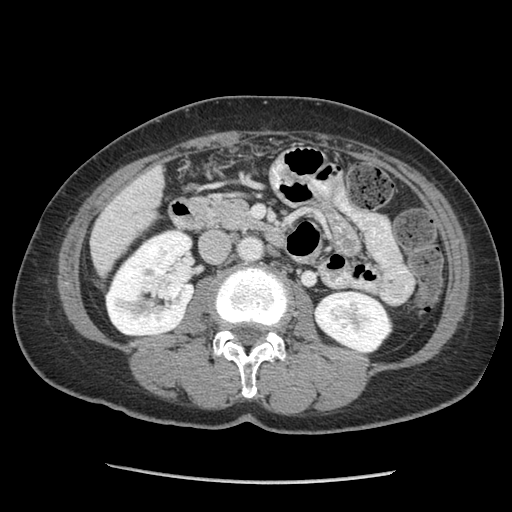
Contrast-enhanced abdominal CT (liver protocol), one axial slice. Slice 22 of 105 in the series (ordered by position). 140 kVp. Soft-tissue window (W 400 / L 40 HU). 2.5 mm slice thickness. 512 × 512 image matrix. From the clinical record (not read from this slice): diagnosis: hepatocellular carcinoma (patient treated with transarterial chemoembolisation; whether this scan precedes or follows treatment is not stated here); TNM stage (as recorded): Stage-I; Child-Pugh class: A; tumour differentiation: moderately differentiated; tumour nodularity: uninodular.
Annotated regions visible in this slice (semi-automatic segmentation, software-assisted and operator-edited):
- liver parenchyma outside the tumour (the mass and vessels are separate outlines, so this box may not span the whole liver): box from (x=90, y=166) to (x=164, y=274) px
- liver vessels: (x=110, y=213)–(x=113, y=240)